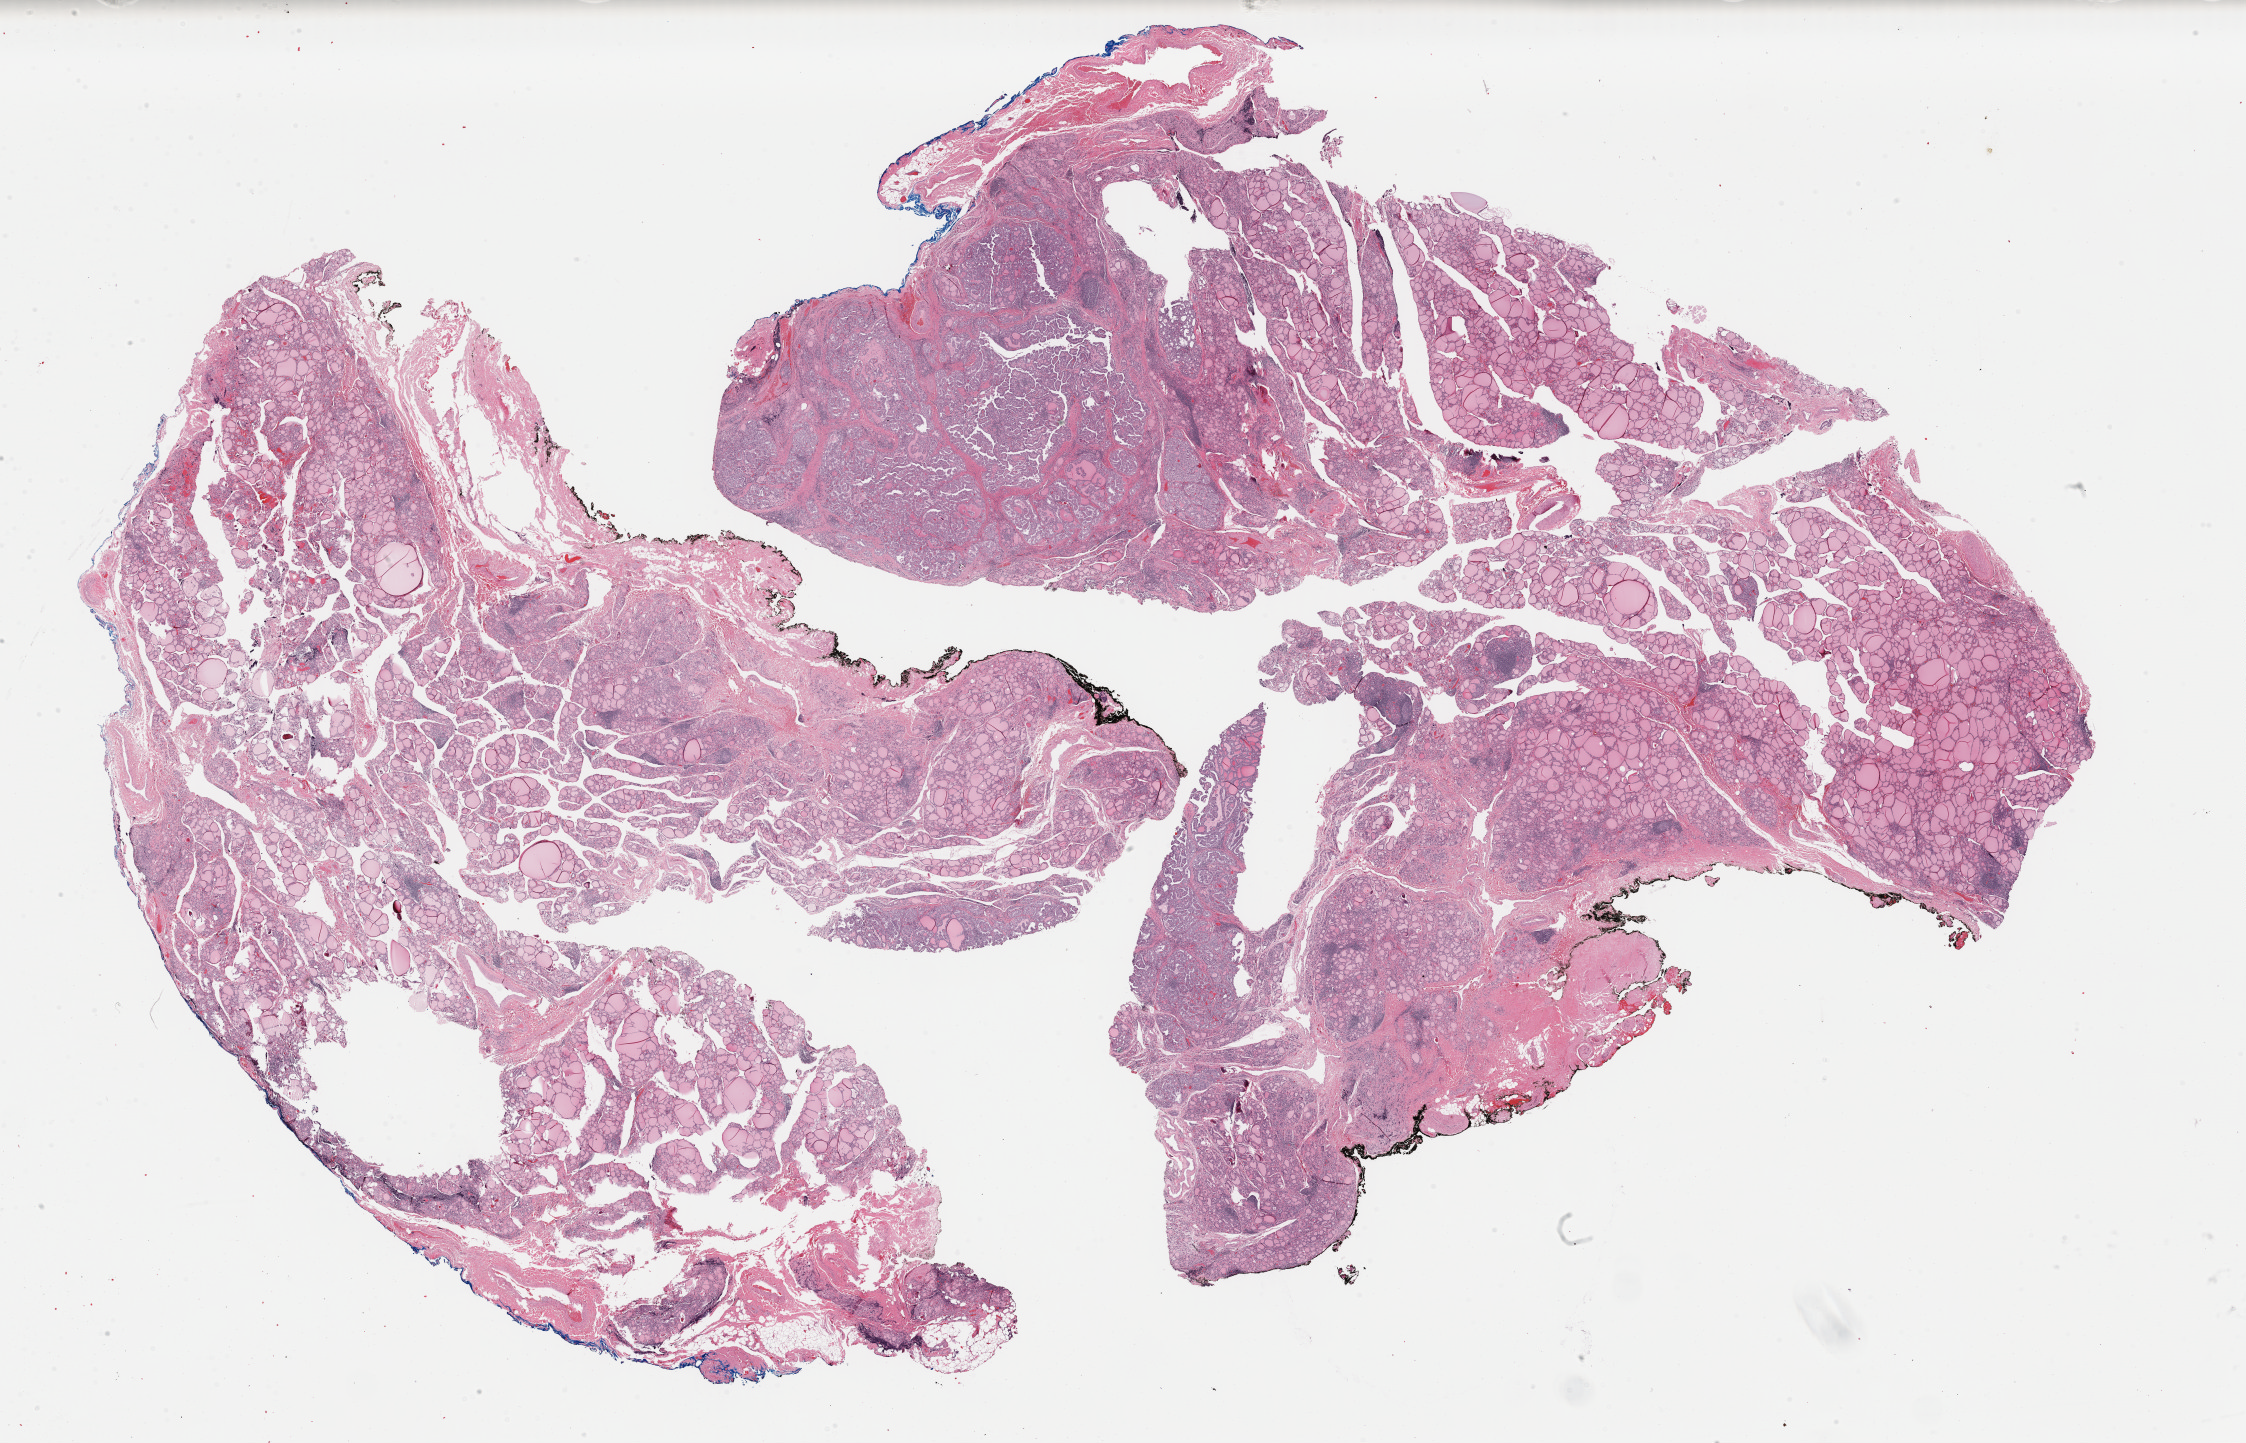
H&E whole-slide image, low-resolution overview of the scanned area, about 35.4 x 22.8 mm. FFPE section. Sample: primary tumour, thyroid. Female, age 36 years at initial diagnosis.
AJCC pathologic stage: I (7th edition). Laterality: left. TNM: T2 N0 M0. Histologic diagnosis: Papillary adenocarcinoma, NOS.